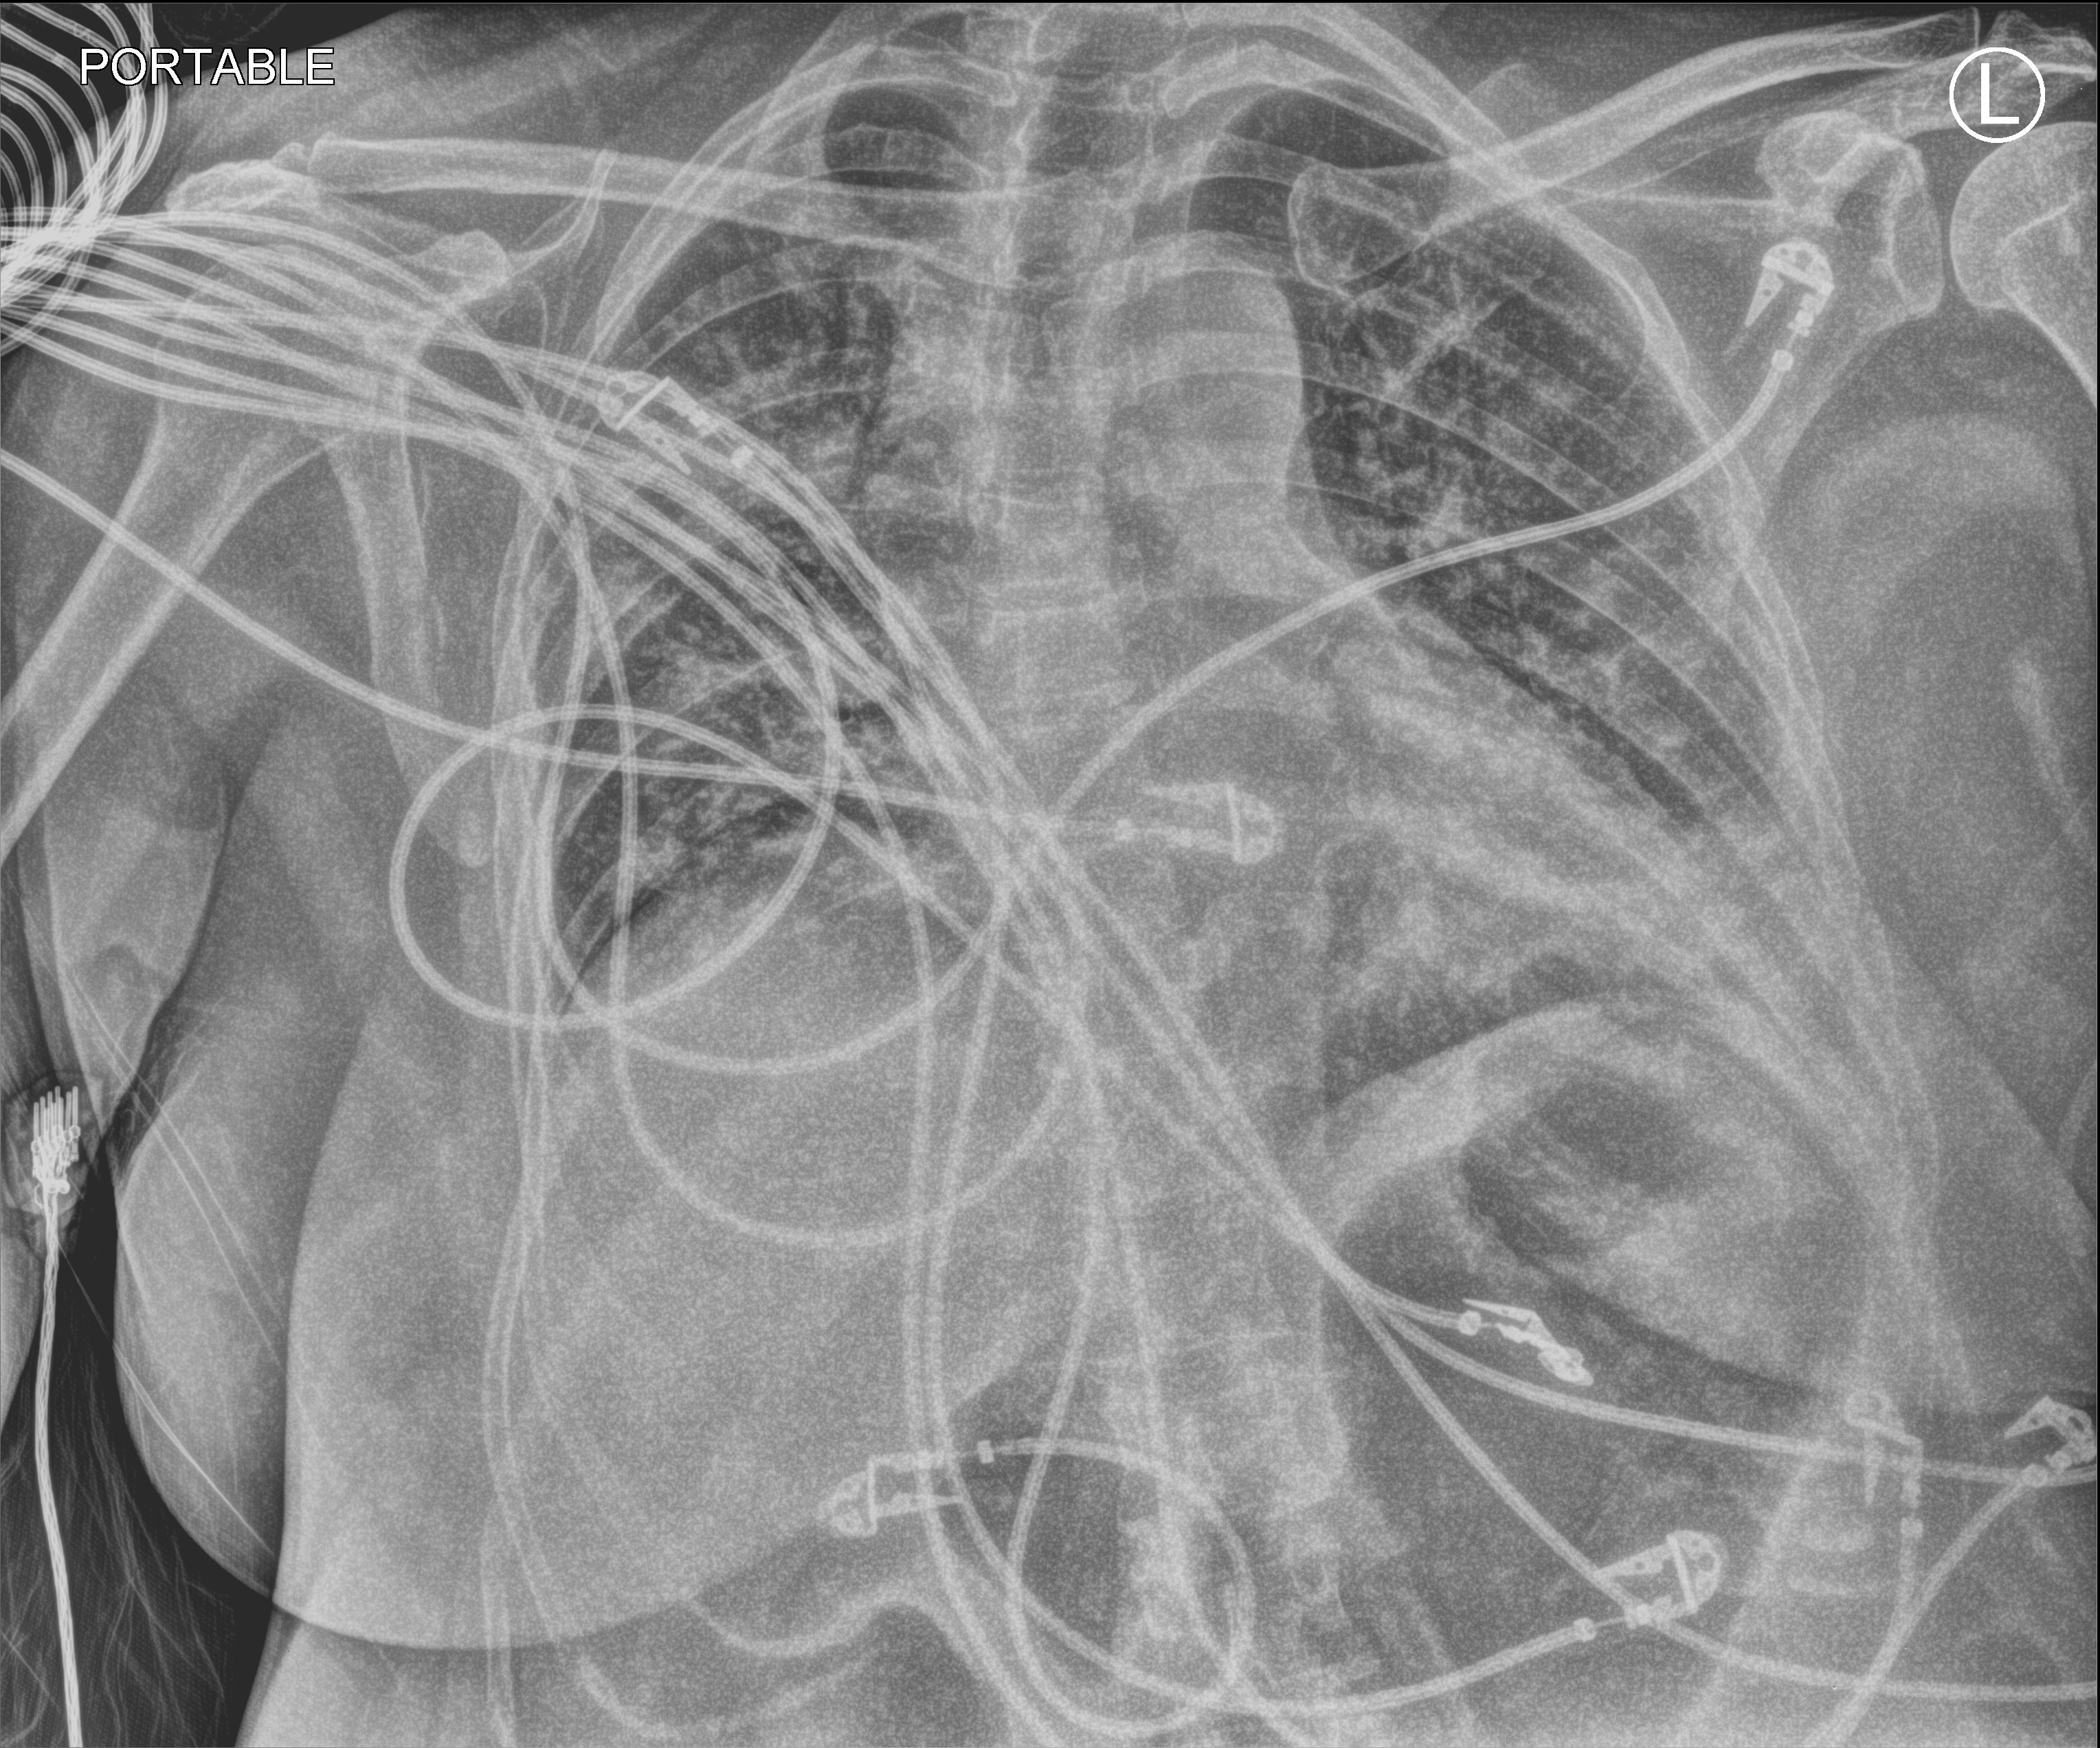
Chest X-ray (portable); anteroposterior (AP) projection. Female patient hospitalised with COVID-19, age 18–59 years.
Admission-level facts for this patient (not findings on this image; timing relative to this image not recorded): mechanically ventilated during this hospital stay: yes.